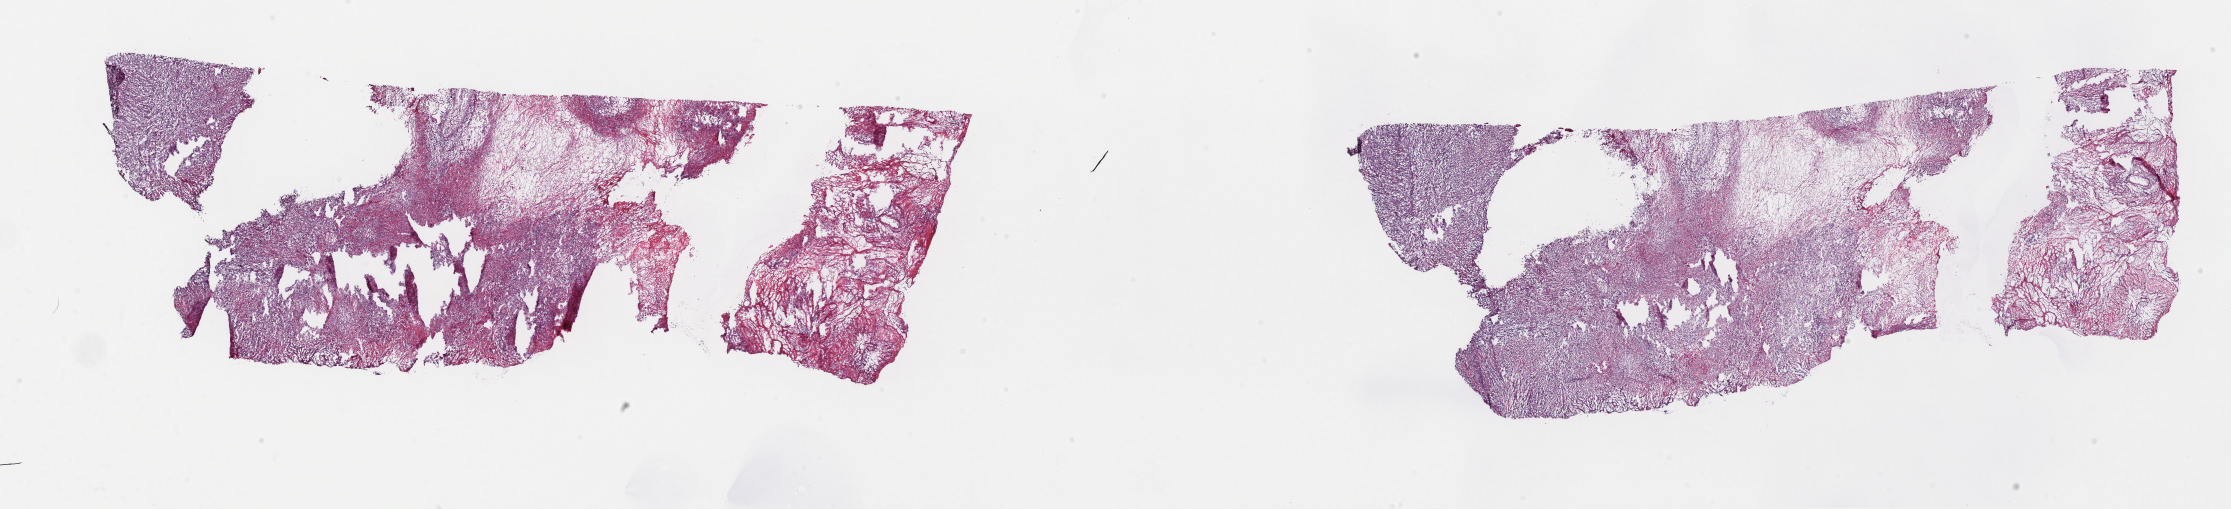
H&E-stained whole-slide image — shown as a low-resolution overview of the whole scanned area (about 35.2 x 8.0 mm, from a 40x scan), frozen section from the top of the tissue portion, sample: primary tumour, connective, subcutaneous and other soft tissues. Patient: male, age at initial diagnosis 62 years. Slide review estimates, as recorded: tumour cells 70%, tumour nuclei 80%, normal cells 0%, stromal cells 30%, necrosis 0%. Infiltration values recorded for this section: lymphocyte infiltration 0%, monocyte infiltration 0%, neutrophil infiltration 0%.
Diagnosis: Dedifferentiated liposarcoma (connective, subcutaneous and other soft tissues of upper limb and shoulder).